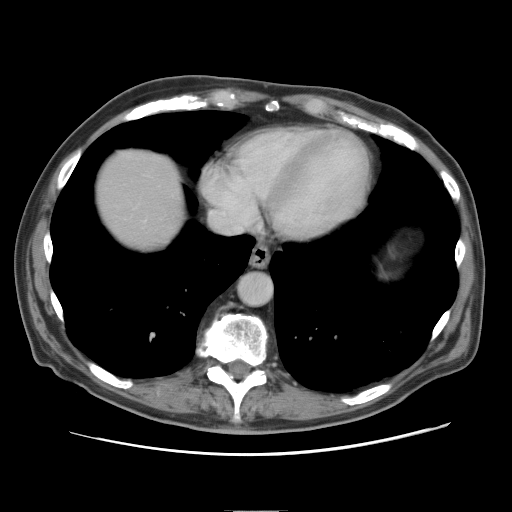
Contrast-enhanced abdominal CT, one axial slice; slice 77 of 89 in the series (ordered by position); 120 kVp; intravenous contrast given; soft-tissue window (W 400 / L 40 HU); 5 mm slice thickness; 512 × 512 image matrix. Male patient, age 69 years. Case-level facts recorded for this patient, not image findings: diagnosis: colorectal cancer liver metastases, imaged before liver resection; multiple liver metastases: no; largest metastasis: 8.5 cm; disease in both lobes: no.
Annotated regions visible in this slice (outlined manually by an expert reader):
- liver: bounding box (x1, y1, x2, y2) in pixels: (97, 149, 184, 252)
- planned liver remnant (the part of the liver to remain after resection): (97, 149, 185, 252)